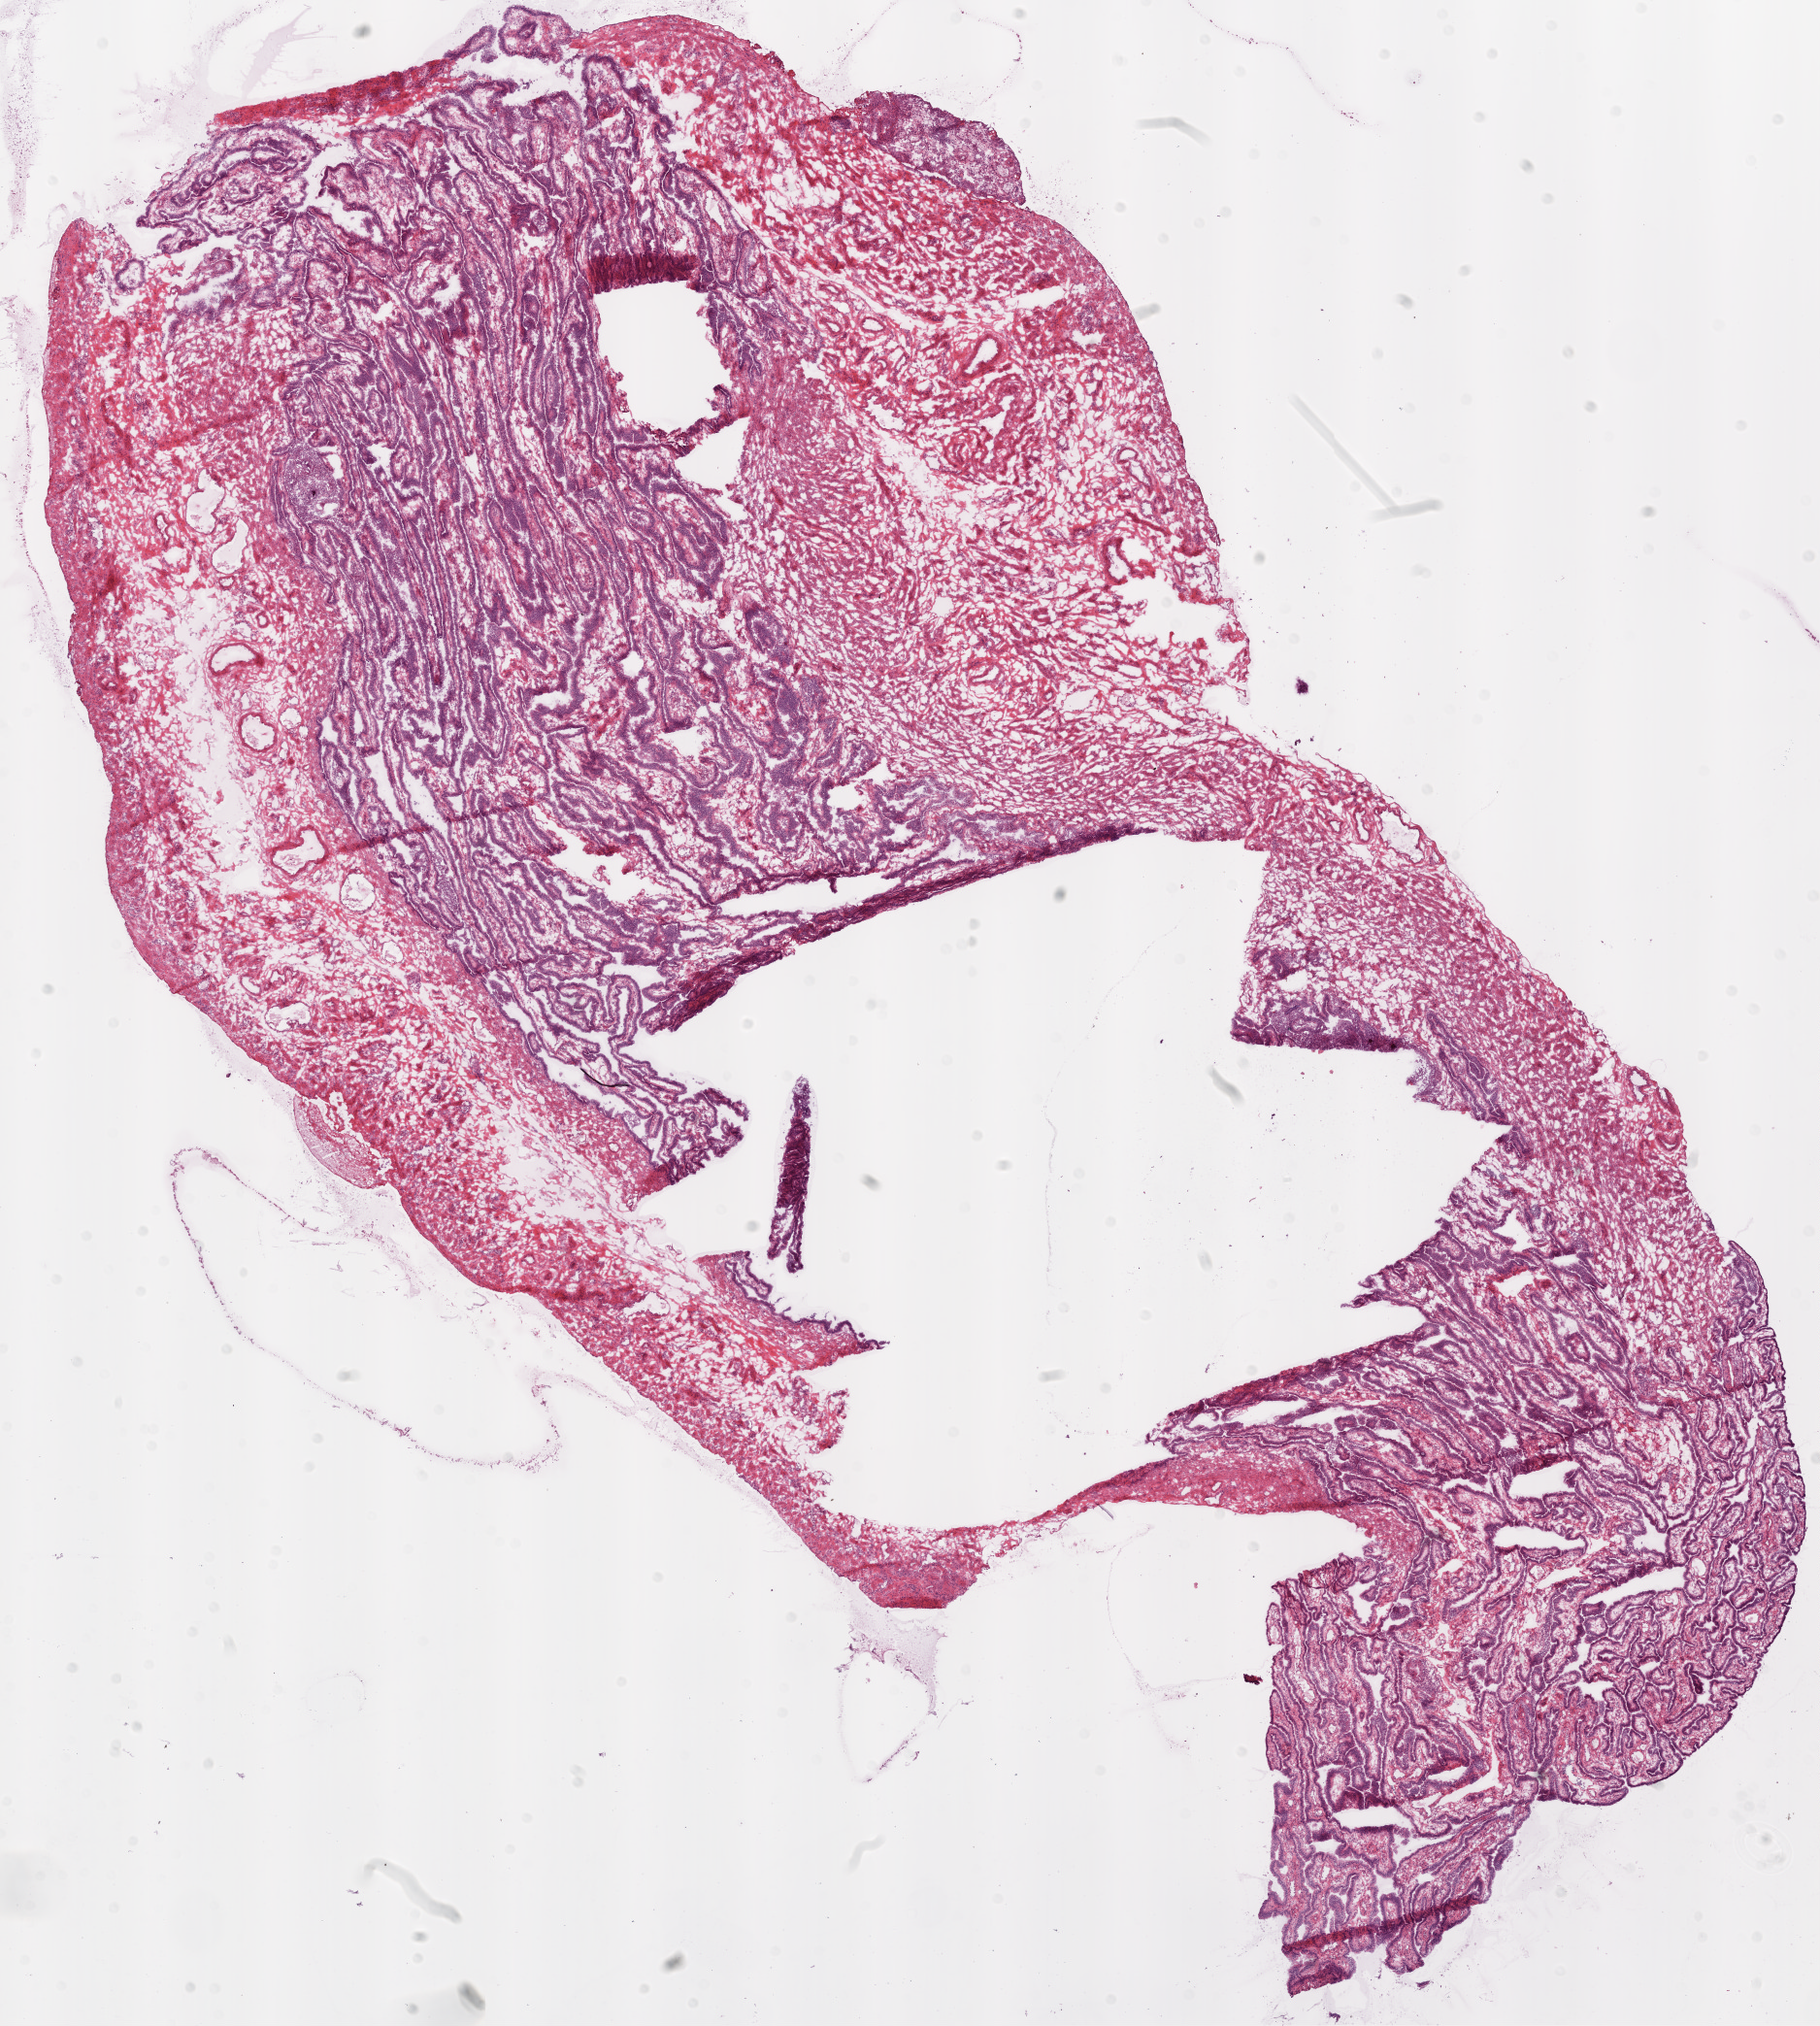
Digitized H&E tissue section (whole slide), shown as a low-resolution overview of the whole scanned area (about 15.0 x 16.7 mm, slide scanned at 20x). Frozen section from the bottom of the tissue portion. Ovary, solid tissue normal (non-tumour tissue) sample. Female, age 43 years at initial diagnosis.
* this section: solid tissue normal sample (biorepository sample class)
* patient diagnosis: Serous cystadenocarcinoma, NOS